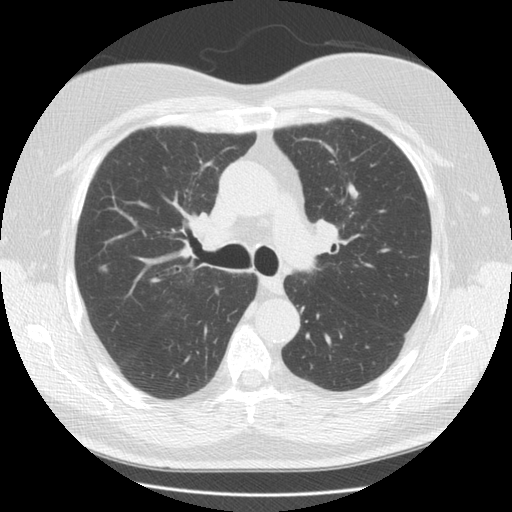
Low-dose screening chest CT, one axial slice; position 93 of 146 along the scan axis; reconstruction kernel STANDARD; lung window (W 1500 / L -600 HU); 2.5 mm slice thickness; 512 × 512 image matrix, field of view 350 × 350 mm.
Outlined on this slice (expert manual segmentation):
- lesion 1 (tumor, upper lobe of right lung): bounding box <98,264,109,274> (left, top, right, bottom; pixels)